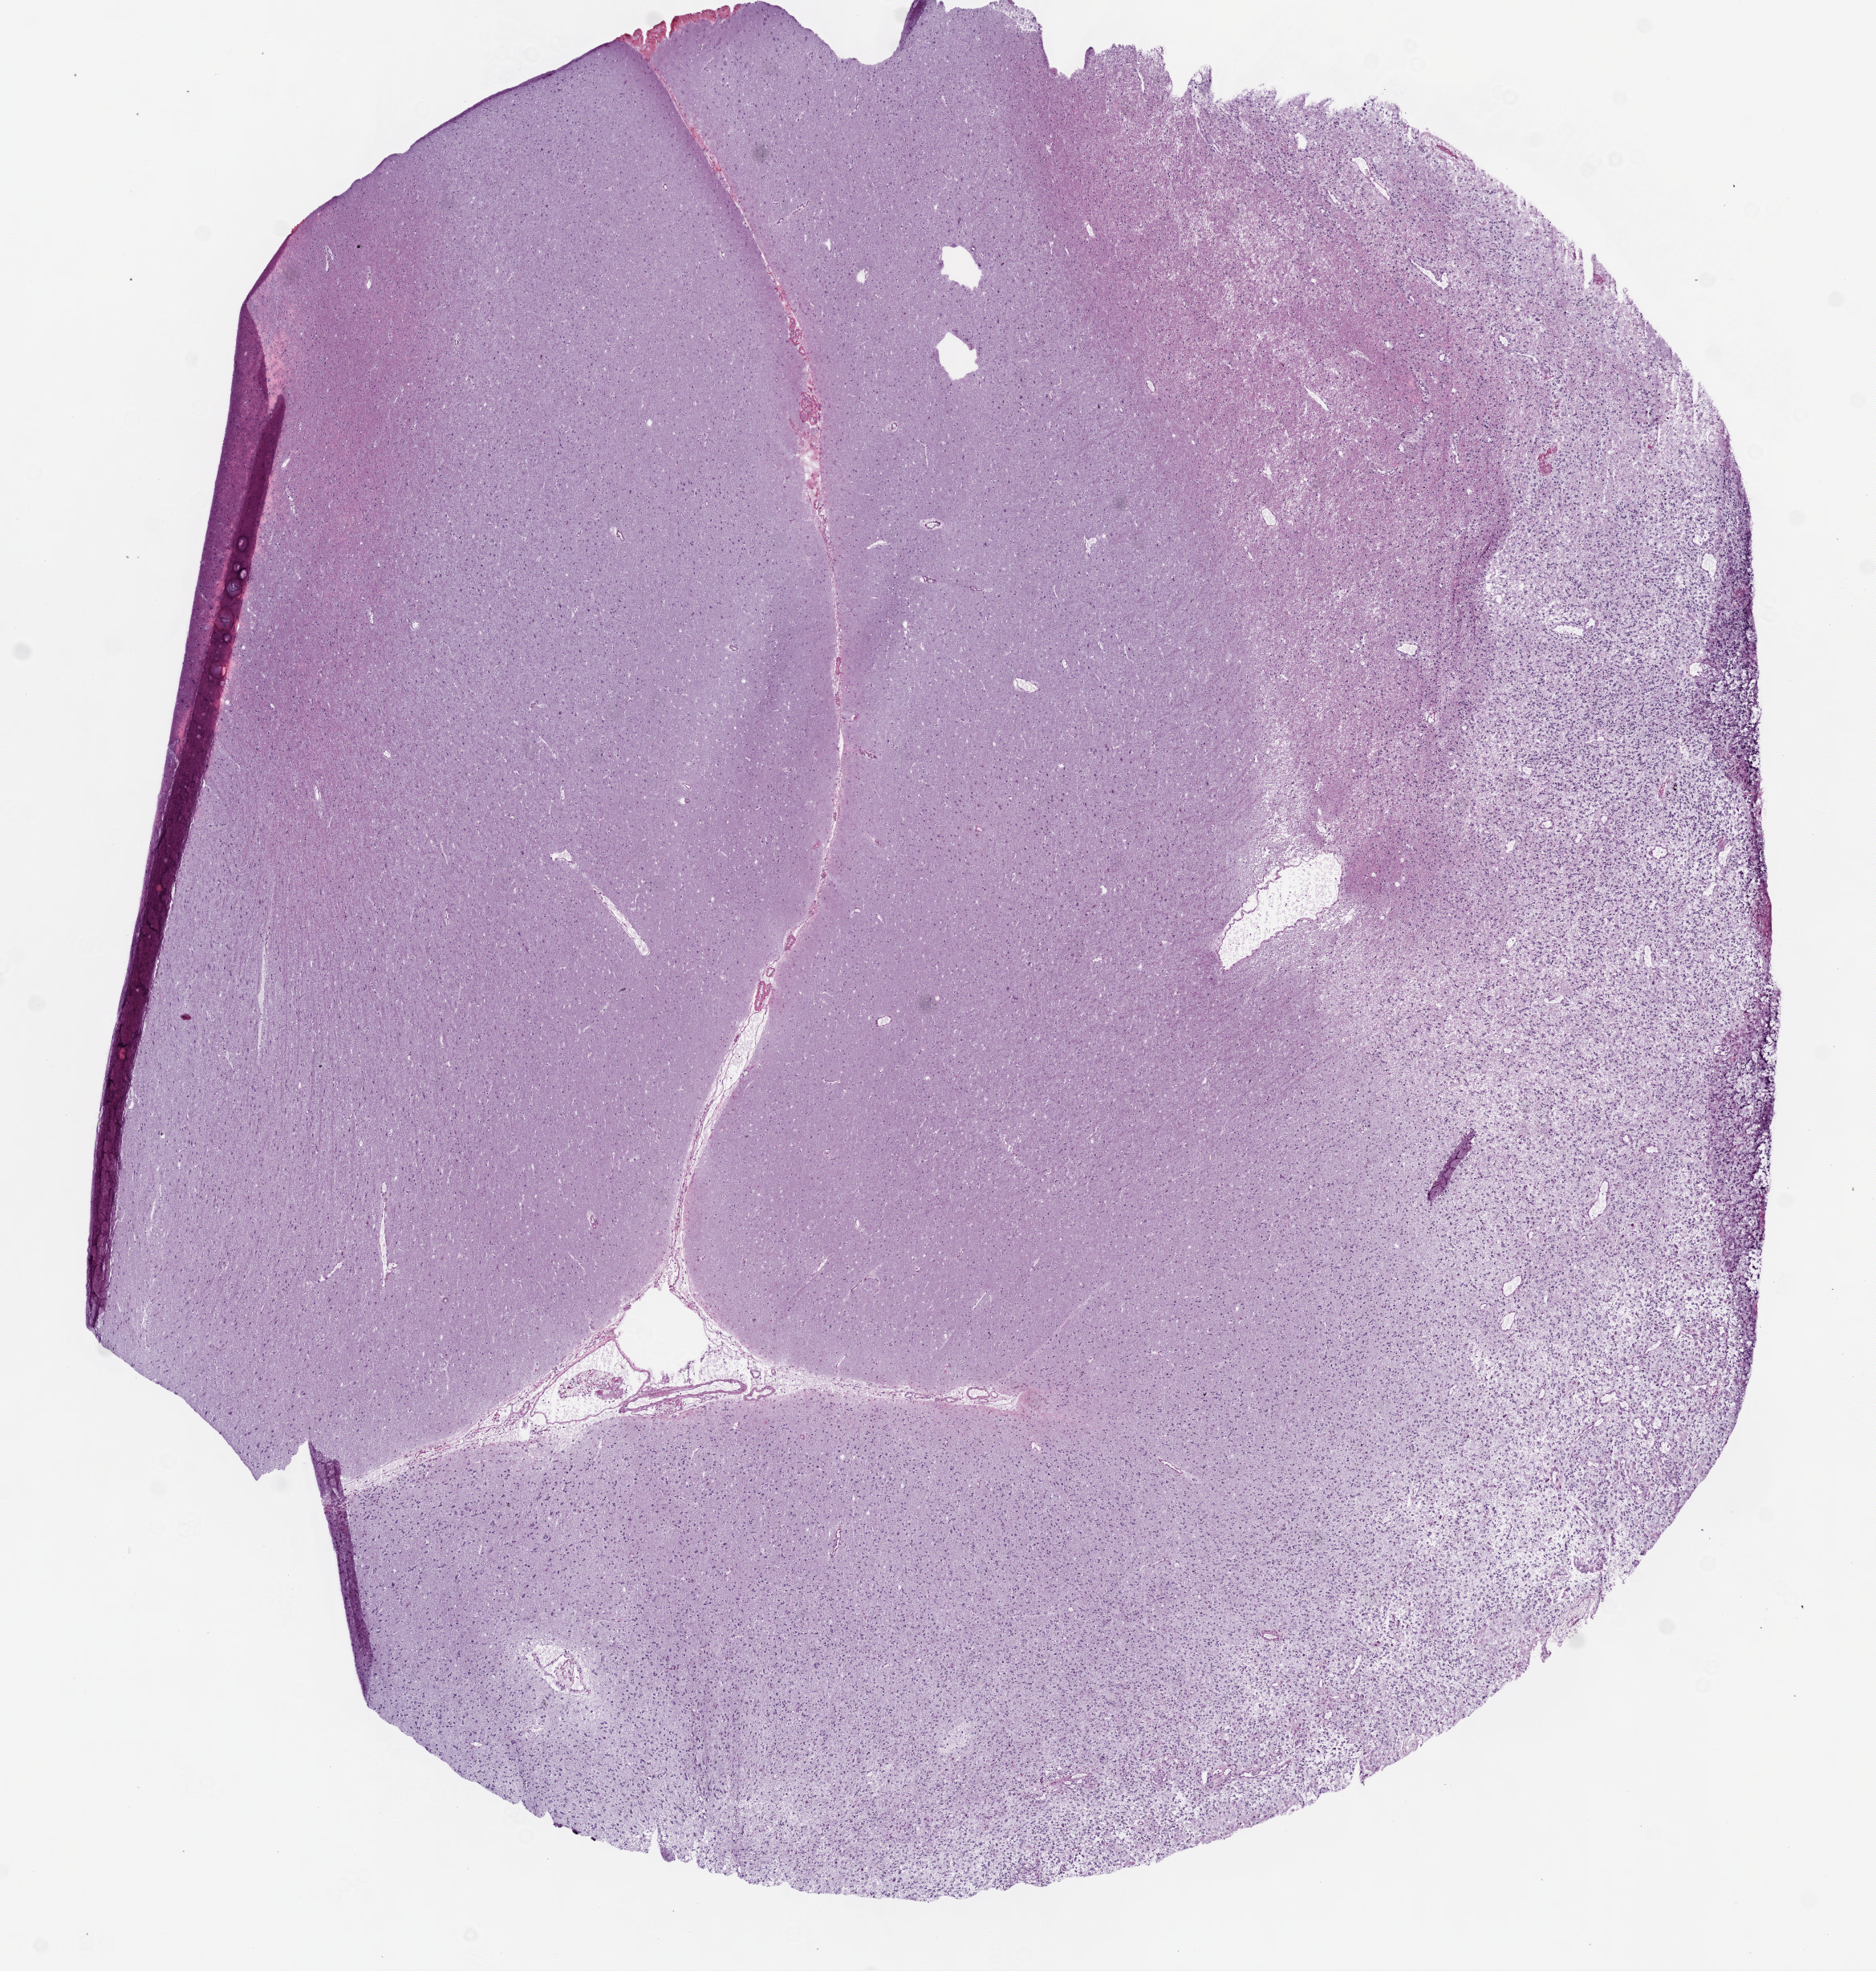
H&E whole-slide image — low-resolution overview of the scanned area, about 9.4 x 9.8 mm; frozen section from the bottom of the tissue portion; primary tumour sample from the brain. Male, age 51 years at initial diagnosis. Pathologist review of this section (percent, as recorded): tumour cells 100%, tumour nuclei 65%, normal cells 0%, stromal cells 0%, necrosis 0%.
Pathologic diagnosis: Glioblastoma.